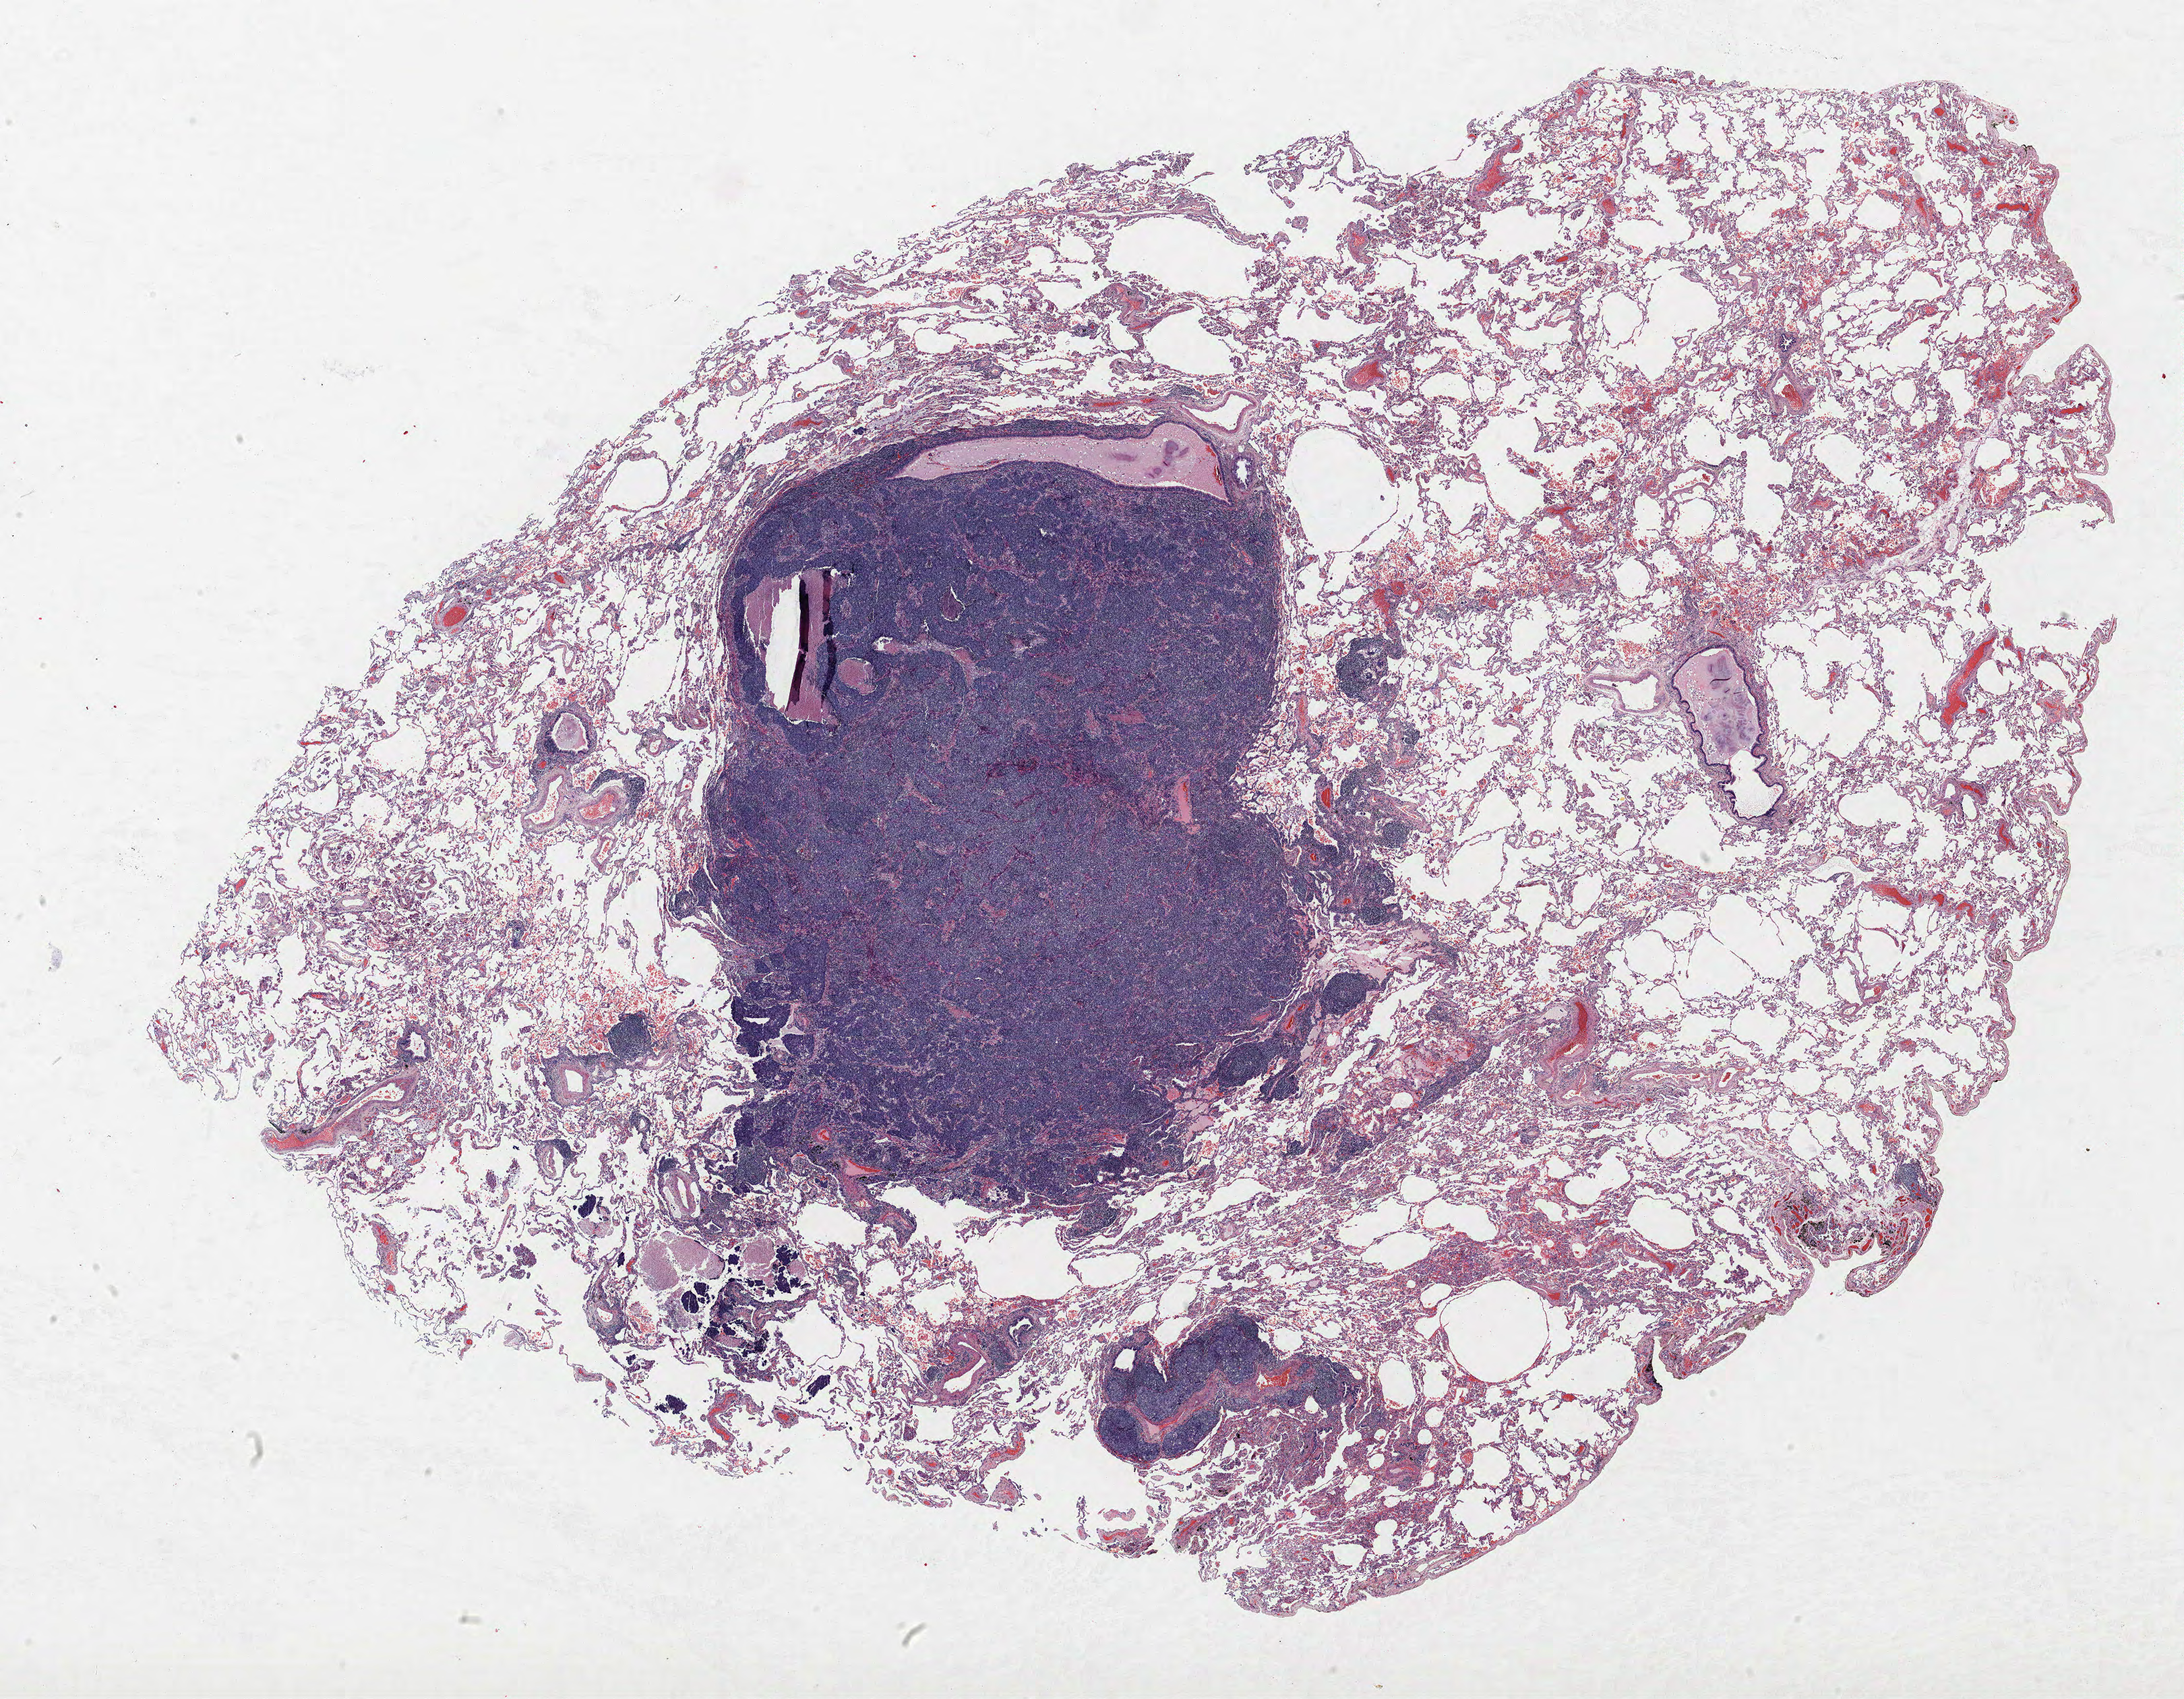
Hematoxylin and eosin (H&E) stained whole-slide image, whole scanned area (about 25.9 x 20.2 mm, acquisition: 40x scan) shown as a low-resolution overview, FFPE section, lung. Female, age 55 at enrolment. Current smoker at enrolment.
- primary tumour location (clinical record): right middle lobe
- tumour size (pathology): 24 mm
- participant's lung-cancer diagnosis: Small cell carcinoma, NOS
- stage (AJCC 6th edition): IIB